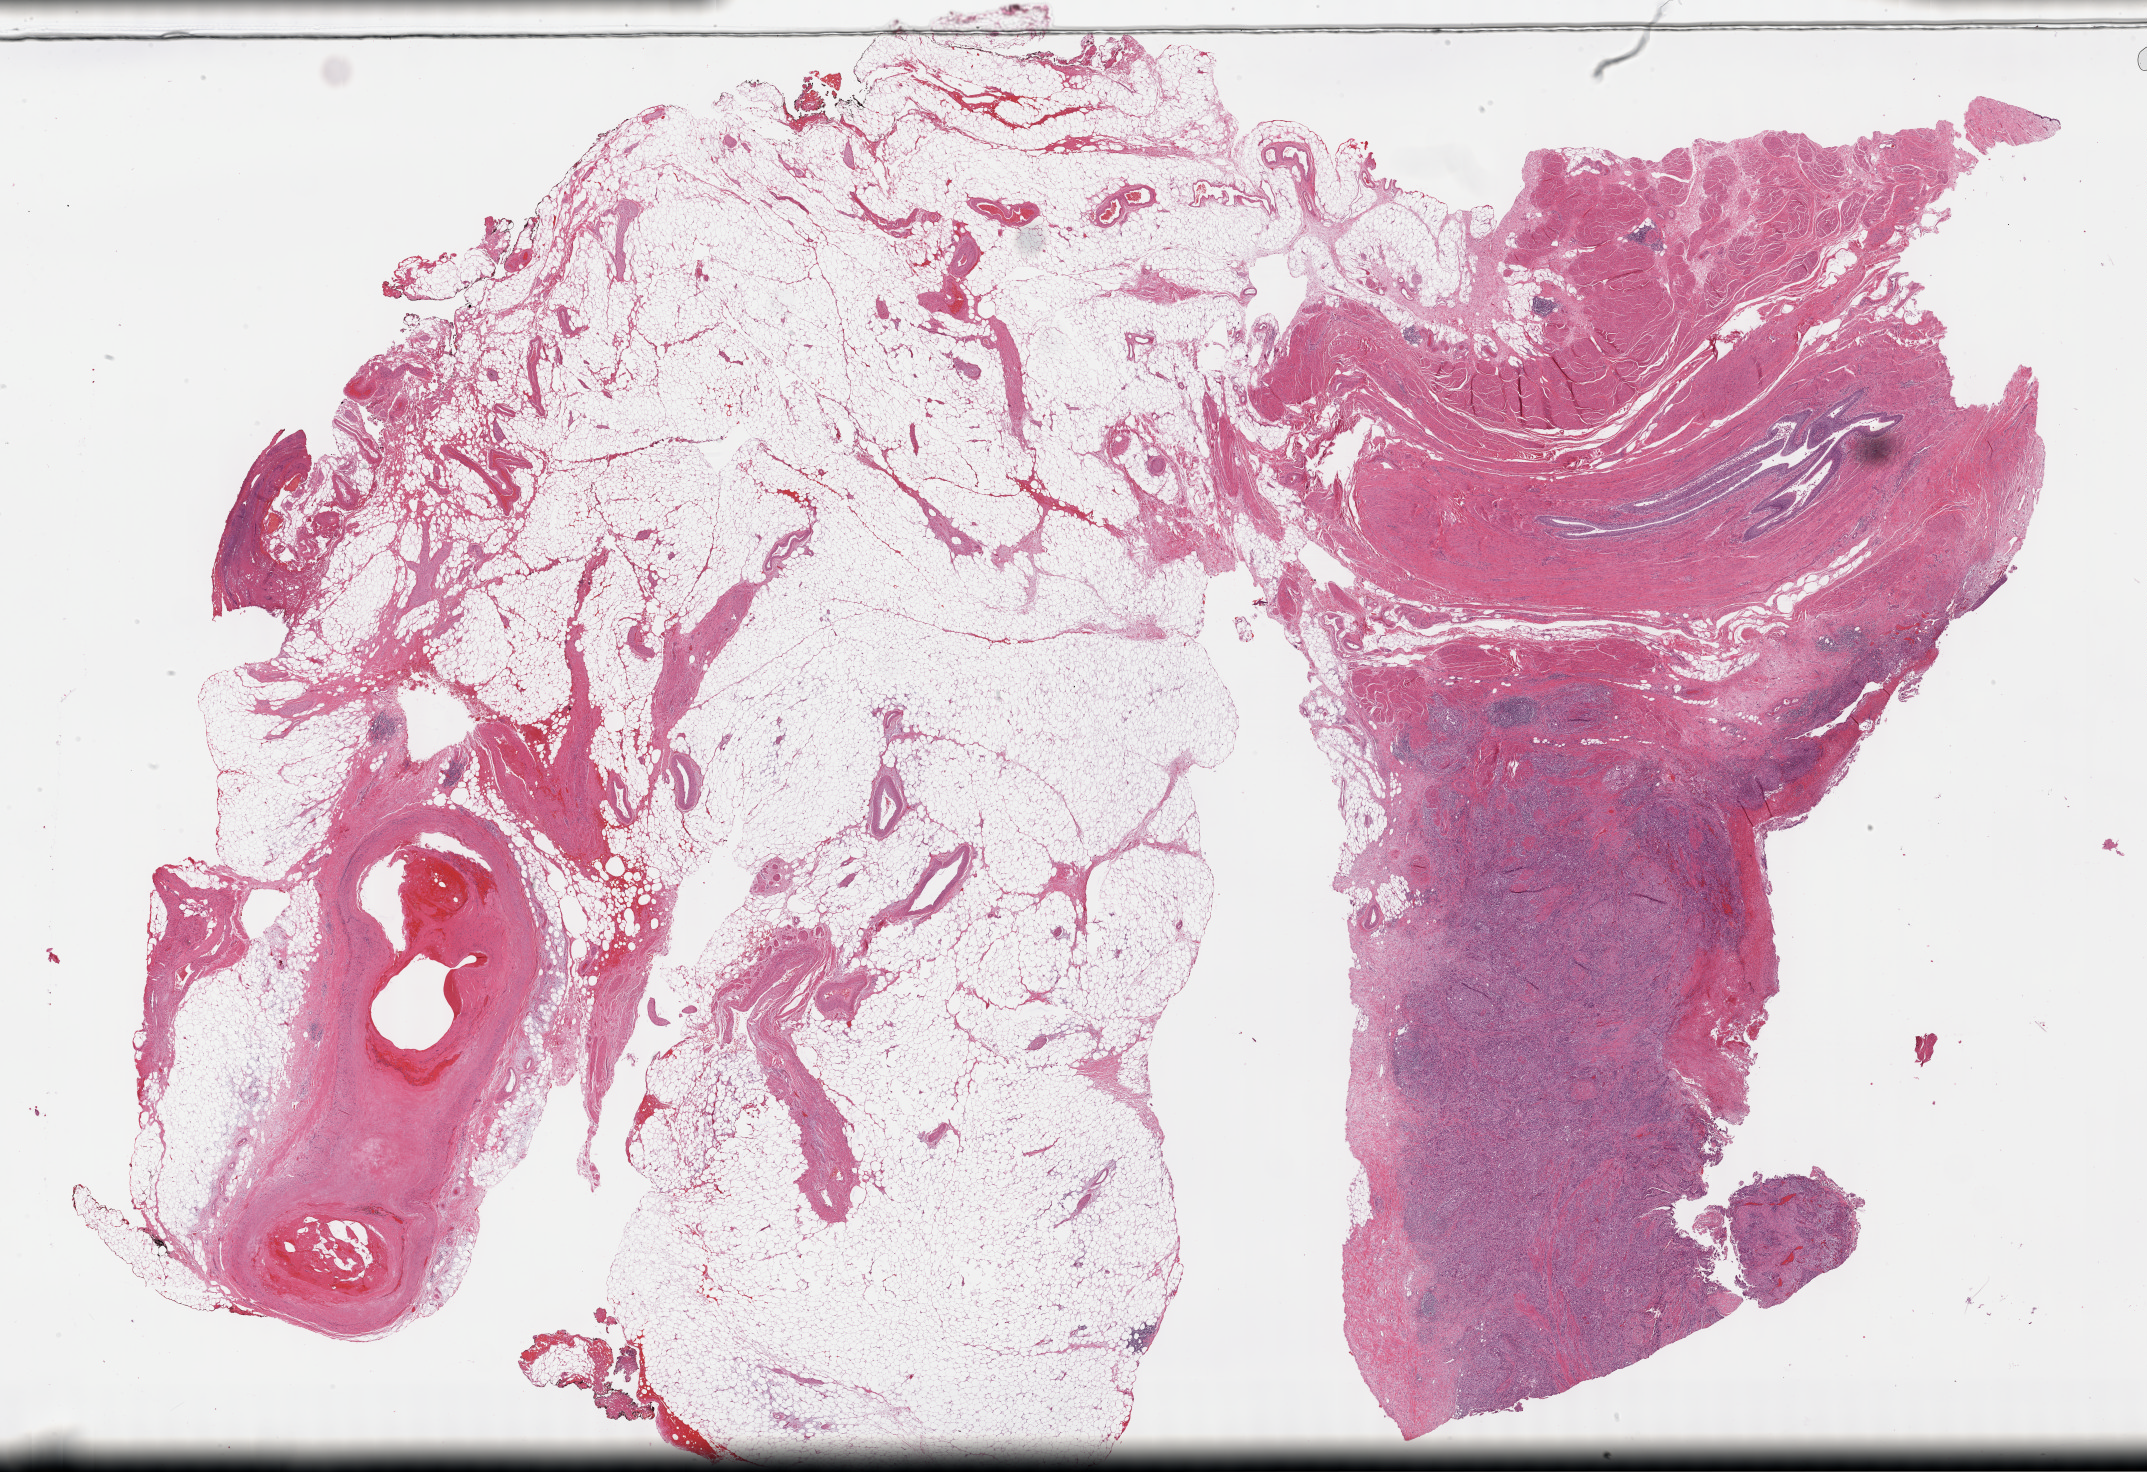
Digitized Hematoxylin and eosin (H&E) stained tissue section (whole slide) — a low-resolution overview of the entire scanned area, about 34.7 x 23.8 mm (slide scanned at 40x); formalin-fixed paraffin-embedded (FFPE) diagnostic section; bladder, primary tumour sample. Patient: female, age at initial diagnosis 61 years.
Diagnosis: Transitional cell carcinoma (posterior wall of bladder).